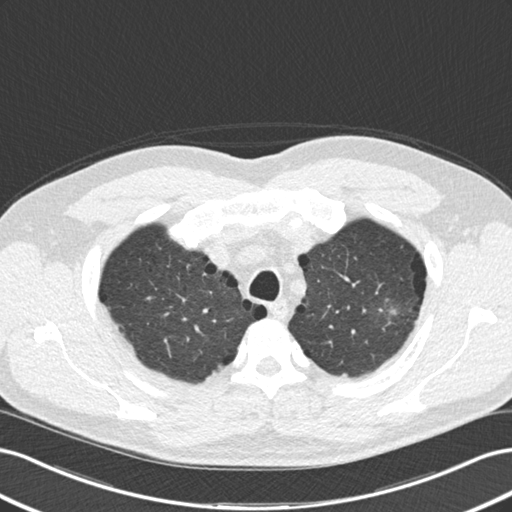
Low-dose screening chest CT, one axial slice. Position 138 of 177 along the scan axis. Lung window (W 1500 / L -600 HU). 2 mm slice thickness. 512 × 512 image matrix, field of view 360 × 360 mm.
Structures marked on this image (expert manual segmentation):
- lesion 1 (tumor, upper lobe of left lung): box from (x=389, y=309) to (x=397, y=315) px